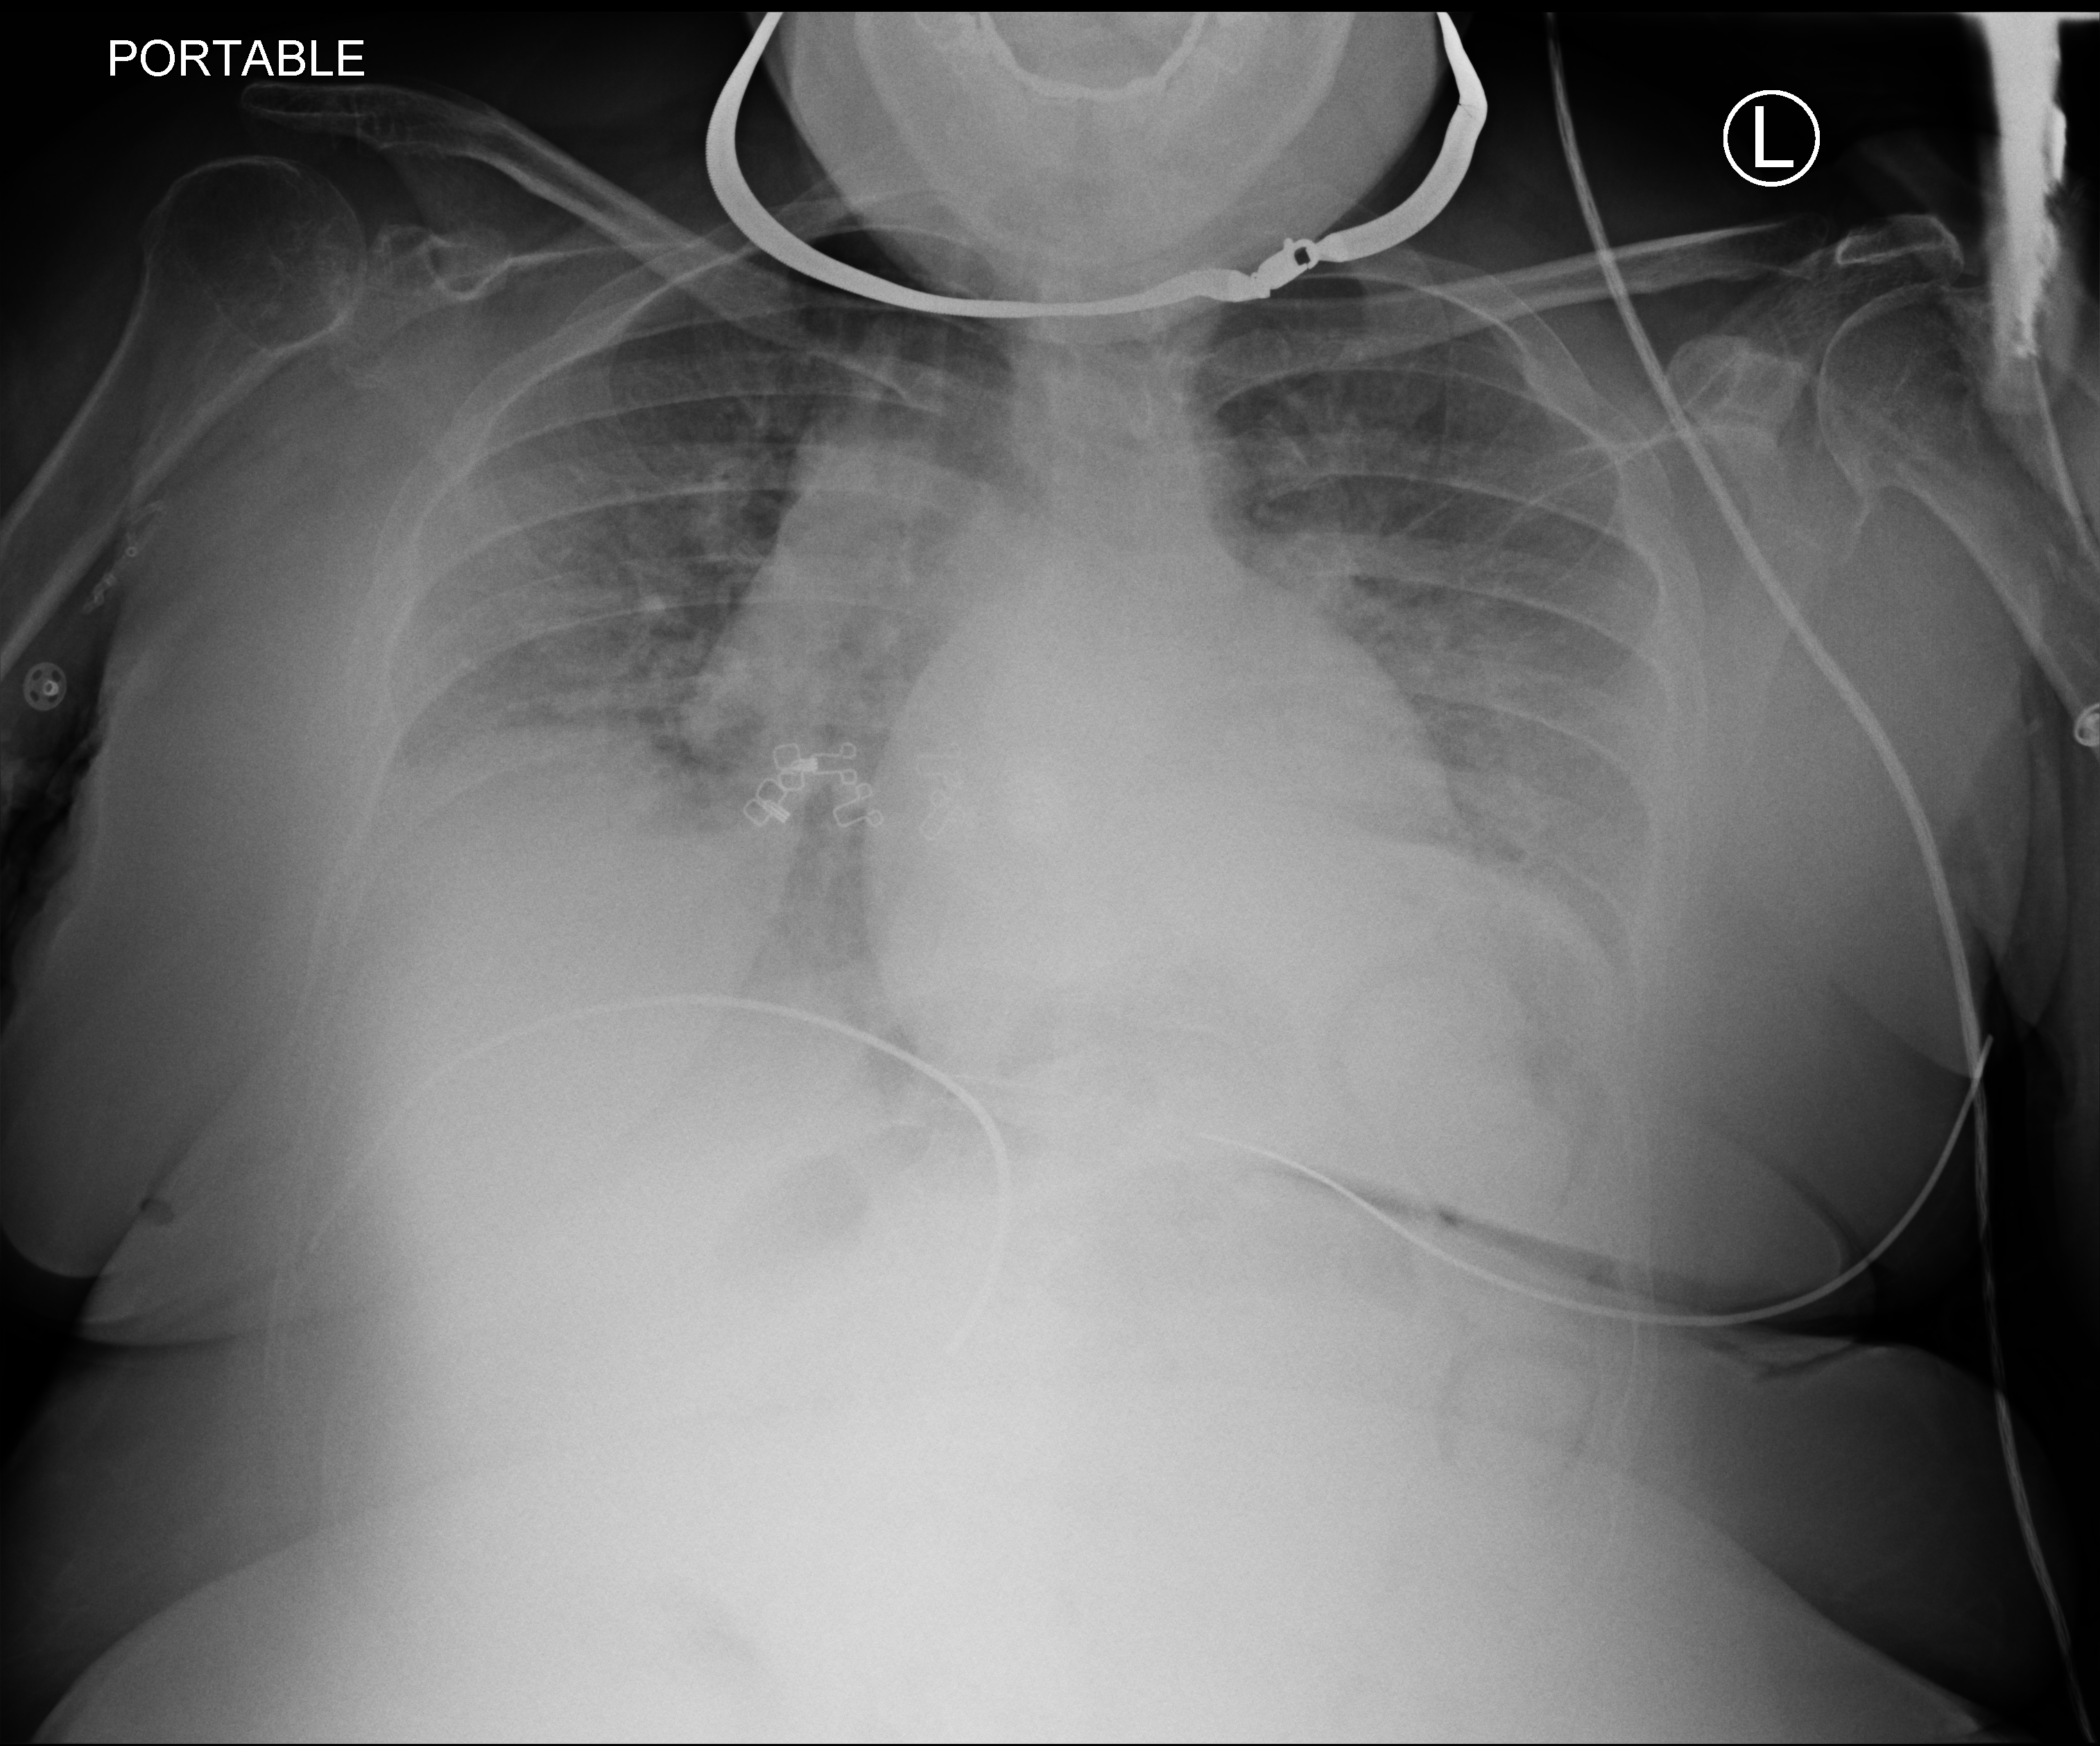
Chest X-ray (portable). Patient hospitalised with COVID-19; female, aged 18–59 years.
From the hospital-stay record, not from the radiograph (when in the stay this image was taken is not recorded):
- hypertension (admission record): no